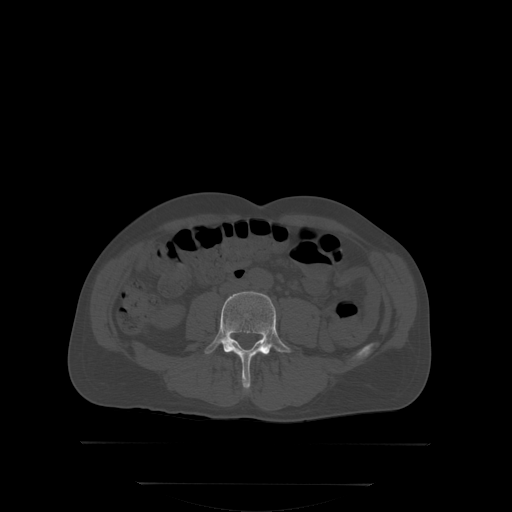
CT including the spine, one axial slice; position 109 of 350 along the scan axis; bone window (W 1800 / L 400 HU); 512 × 512 image matrix. Patient: male, 58 years. From the clinical record (not read from this slice): primary cancer: prostate; vertebrae with lytic lesions (as recorded): L1.
Structures marked on this image (semi-automatically segmented with operator editing):
- L4 vertebra: bounding box [x1, y1, x2, y2] px = [204, 291, 291, 390]